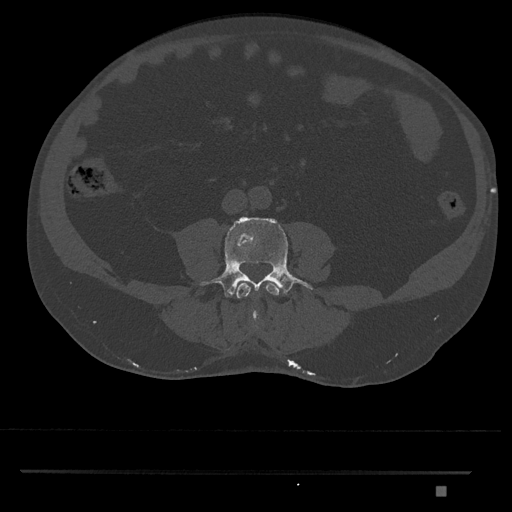
CT including the spine, one axial slice; slice 633 of 1134 in the series (ordered by position); reconstruction kernel Br40s/3; bone window (W 1800 / L 400 HU); 512 × 512 image matrix, field of view 429 × 429 mm. Male patient, age 65 years. Case-level facts recorded for this patient, not image findings: primary cancer: prostate.
Structures marked on this image (semi-automatic segmentation, software-assisted and operator-edited):
- L3 vertebra: bounding box <236,282,279,323> (left, top, right, bottom; pixels)
- L4 vertebra: <200,217,313,316>